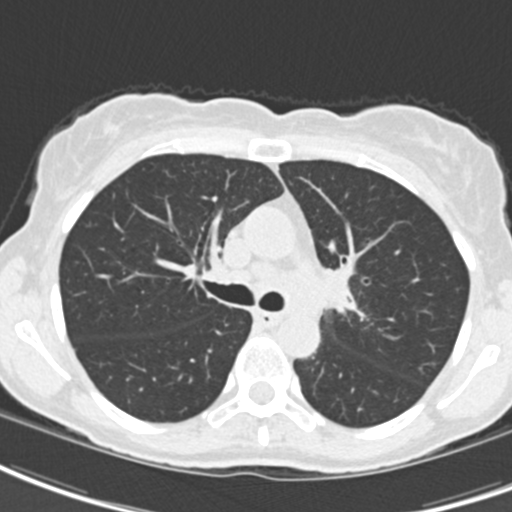
Chest CT (low-dose screening protocol), one axial image; baseline annual screen; lung window (W 1500 / L -600 HU); slice 60 of 189 in the series; 512 × 512 image matrix, field of view 279 × 279 mm. Female participant, aged 62 years at enrolment. Current smoker at enrolment.
Lesion marked by an expert reader, bounding box <294,250,368,334> (left, top, right, bottom; pixels). Reader record for this screening exam (exam-level; its link to the box is not recorded): non-calcified nodule or mass ≥4 mm, right upper lobe, 24 × 20 mm, smooth margins, ground glass attenuation. Note: the box lies in the patient's left hemithorax on this image, whereas the reader's record names the right lung; they may be different findings. Lung cancer was diagnosed 24 days after this screen: oat cell carcinoma, left hilum, left main stem bronchus, stage IIIB (AJCC 6th edition), 50 mm at pathology.